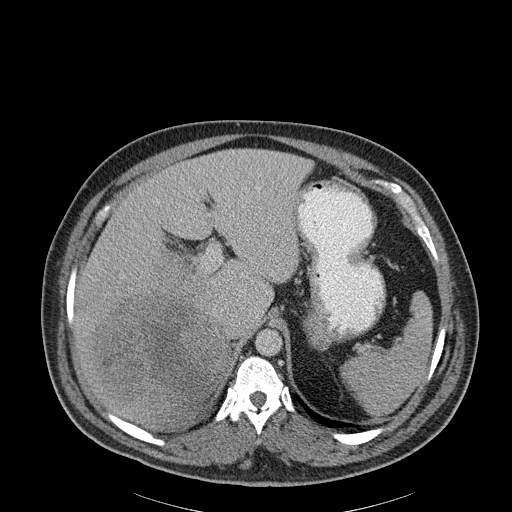
Contrast-enhanced abdominal CT, one axial slice. Slice 145 of 186 in the series (ordered by position). Reconstruction kernel B30f. Soft-tissue window (W 400 / L 40 HU). 3 mm slice thickness. 512 × 512 image matrix. Male patient, age 56 years. From the clinical record (not read from this slice): diagnosis: adrenocortical carcinoma; tumour side: right adrenal; tumour size at pathology: 18 cm; Ki-67 index: 2 %; stage (as recorded): 3.
Outlined on this slice (semi-automatic segmentation, software-assisted and operator-edited):
- mass: box from (x=98, y=265) to (x=222, y=406) px